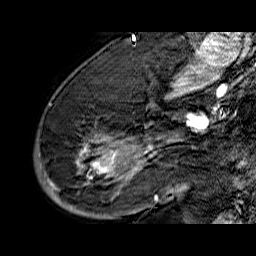
Breast MRI (dynamic contrast-enhanced), one sagittal slice. Slice 41 of 60 in the series (ordered by position). Dynamic contrast-enhanced series, time point 2 of 6 at this slice position (early post-contrast). 1.5 T. TE 6.5 ms, TR 32.9 ms. 4 mm slice thickness. 256 × 256 image matrix, field of view 200 × 200 mm. Female patient. From the clinical record (not read from this slice): setting: breast cancer imaged before/during neoadjuvant chemotherapy; receptor status: HR-positive, HER2-negative.
Structures marked on this image (semi-automatically segmented with operator editing):
- analysis volume of interest (the breast-tissue region the enhancement analysis was run in; not a lesion): bounding box [x1, y1, x2, y2] px = [34, 74, 176, 210]
- tumour enhancement mask (voxels above the 100 % enhancement threshold inside the analysis volume of interest): [38, 136, 176, 202]